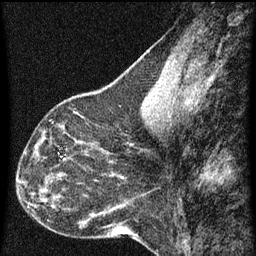
Breast MRI (dynamic contrast-enhanced), one sagittal slice. Position 28 of 60 along the scan axis. Dynamic contrast-enhanced series, image 2 of 3 at this slice position (ordered by acquisition). 1.5 T. TE 4.2 ms, TR 8 ms. 256 × 256 image matrix, field of view 180 × 180 mm. Female patient, age 44 years.
Outlined on this slice (semi-automatic segmentation, software-assisted and operator-edited):
- analysis volume of interest (the breast-tissue region the enhancement analysis was run in; not a lesion): bounding box (x1, y1, x2, y2) in pixels: (49, 128, 95, 169)
- tumour enhancement mask (voxels above the 70 % enhancement threshold inside the analysis volume of interest): (72, 140, 87, 157)